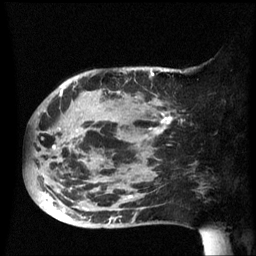
Breast MRI (dynamic contrast-enhanced), one sagittal slice; dynamic contrast-enhanced series, image 2 of 3 at this slice position (ordered by acquisition); 1.5 T; TE 4.2 ms, TR 8.4 ms; 2.5 mm slice thickness; 256 × 256 image matrix. Female patient, age 49 years.
Structures marked on this image (semi-automatic segmentation, software-assisted and operator-edited):
- analysis volume of interest (the breast-tissue region the enhancement analysis was run in; not a lesion): bounding box <25,72,184,229> (left, top, right, bottom; pixels)
- tumour enhancement mask (voxels above the 70 % enhancement threshold inside the analysis volume of interest): <54,72,174,225>